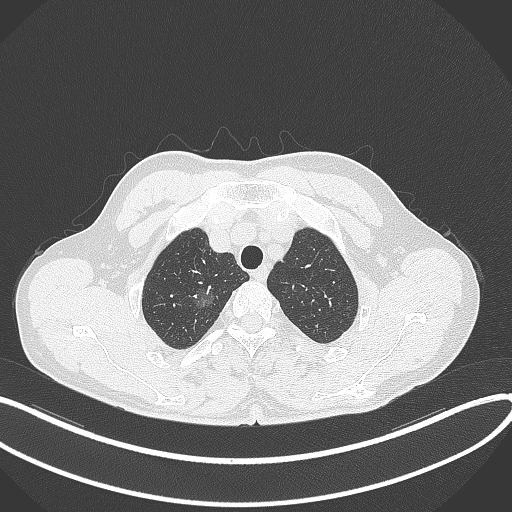
Chest CT, one axial slice. Slice 325 of 407 in the series (ordered by position). Reconstruction kernel B70f. Lung window (W 1500 / L -600 HU). 1 mm slice thickness. 512 × 512 image matrix. Patient: male, 58 years. From the clinical record (not read from this slice): clinical TNM (as recorded): T1c N0 M0; histopathological grade: G1-2.
Annotated regions visible in this slice (bounding box drawn by a radiologist):
- lung tumour (recorded histology: adenocarcinoma): bounding box <189,280,217,313> (left, top, right, bottom; pixels)